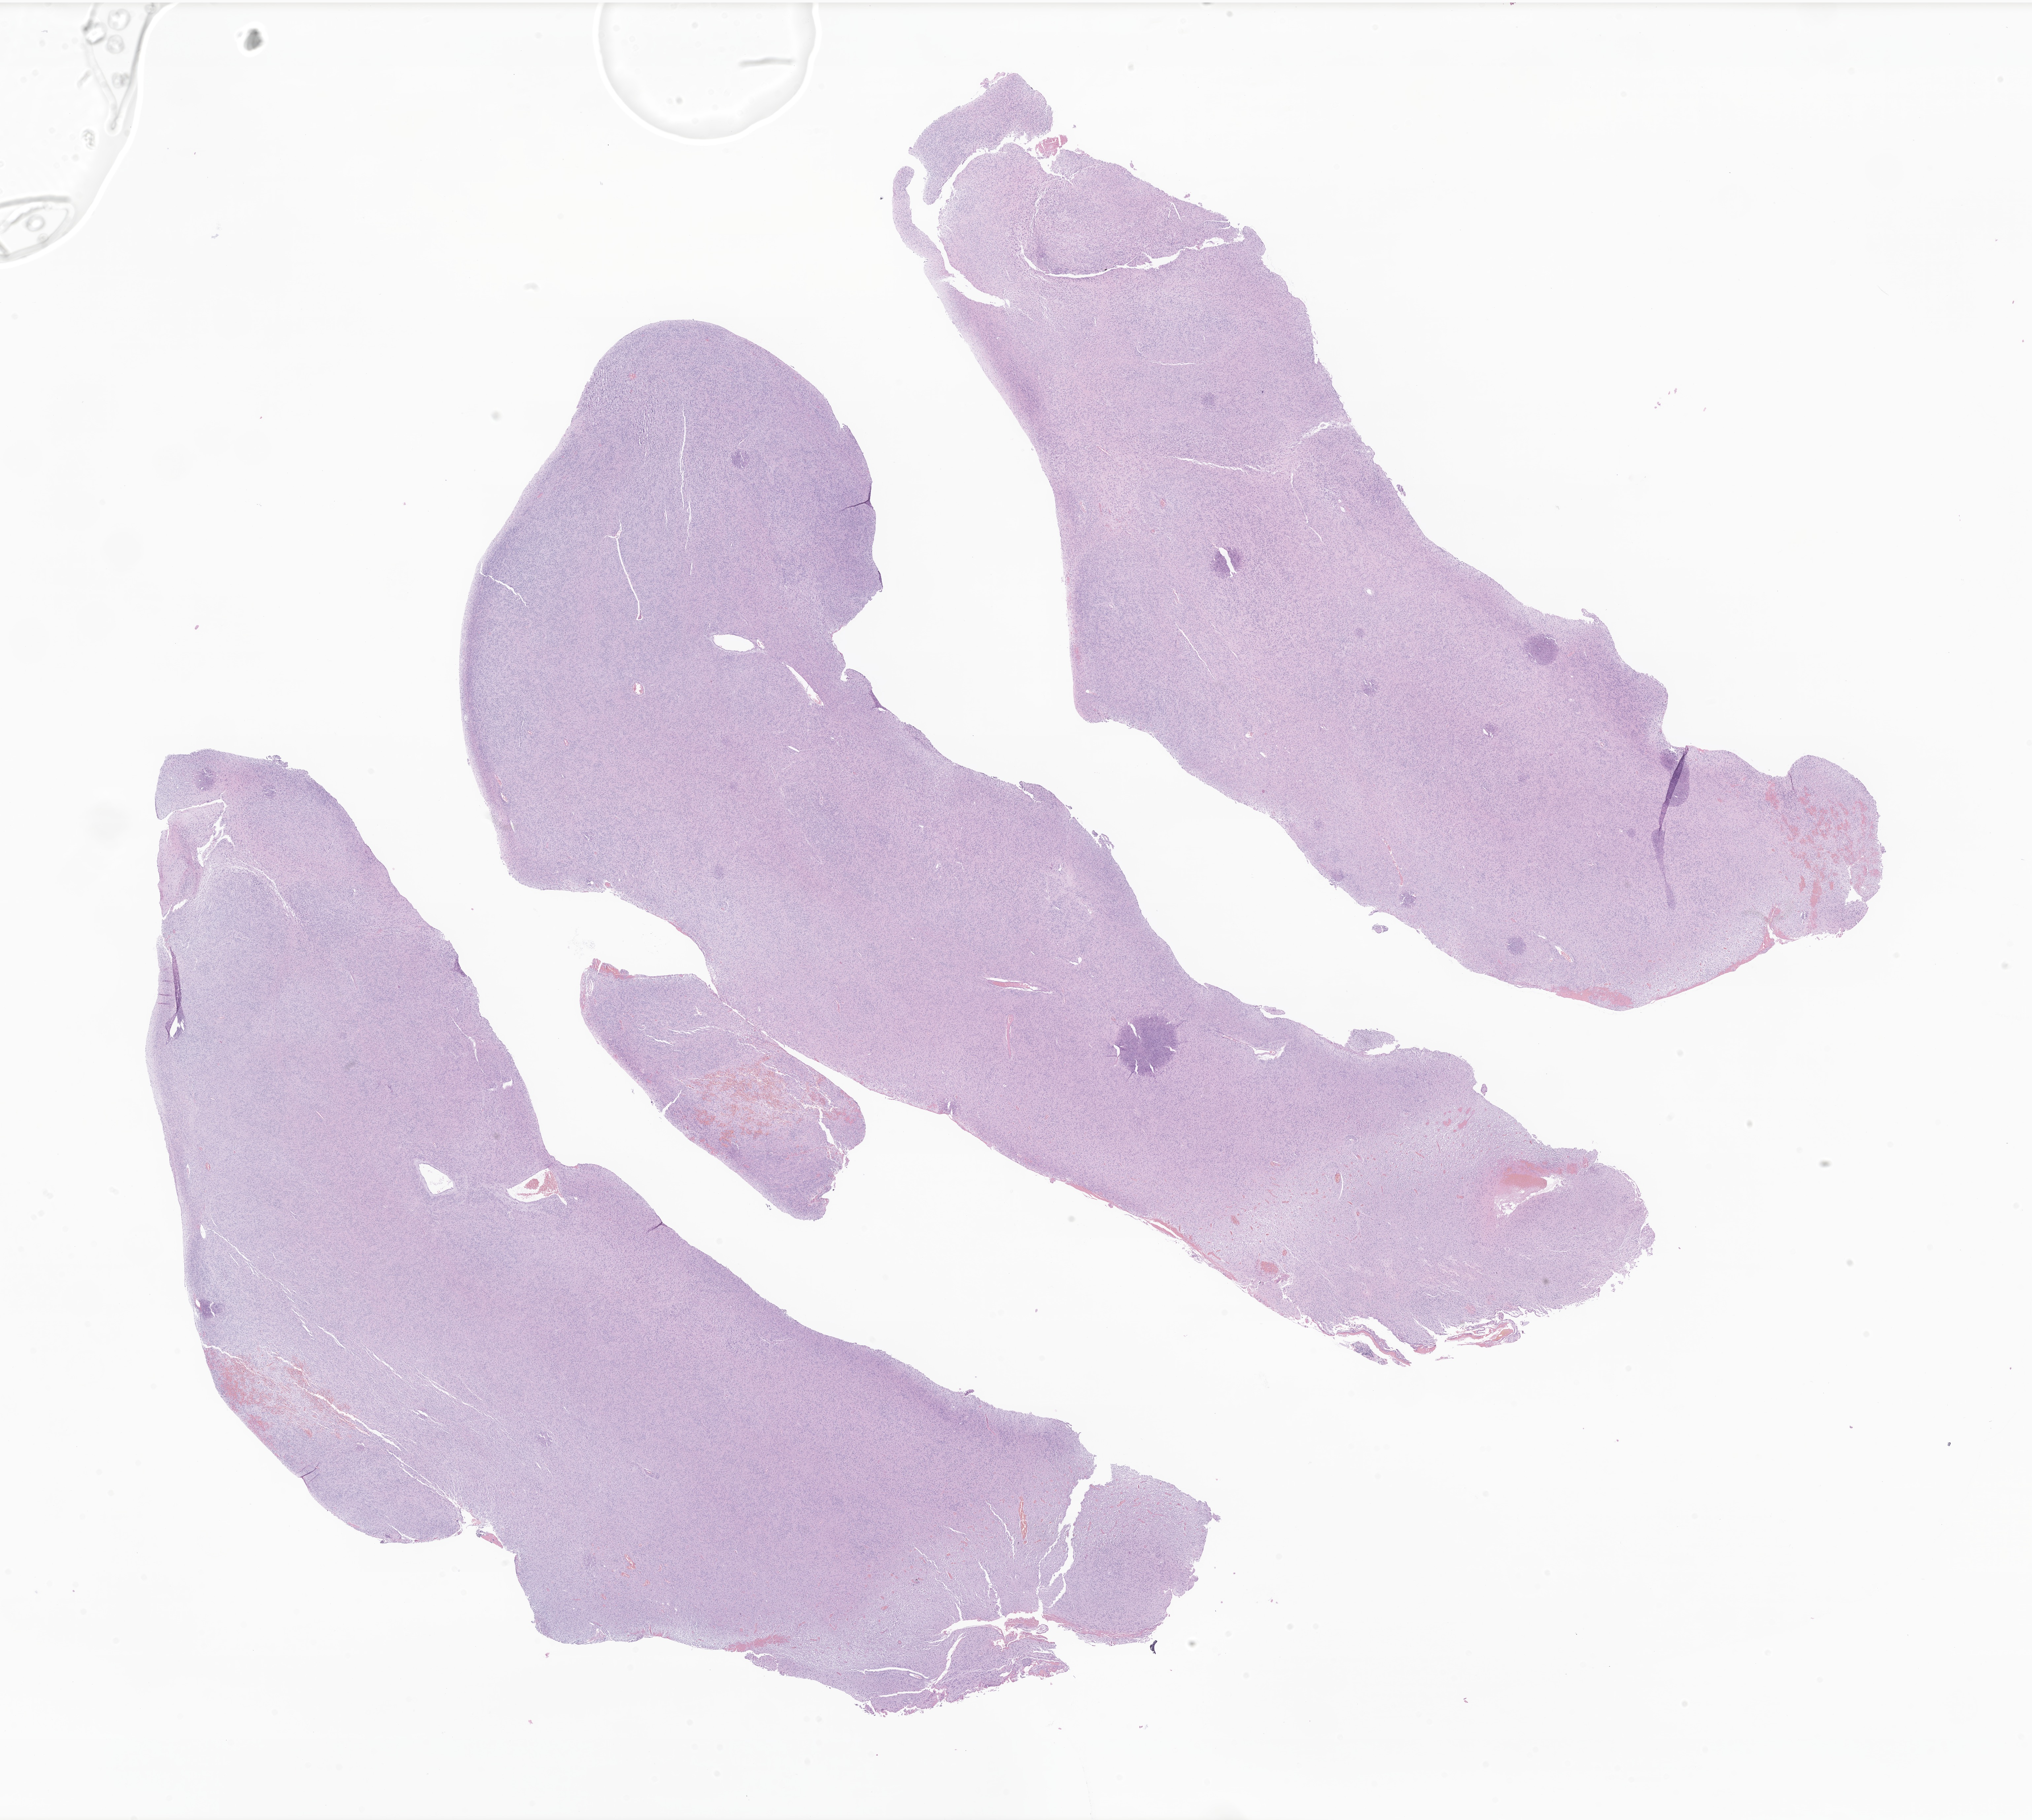
Digitized hematoxylin and eosin (H&E)-stained section of tumor tissue from the brain stem — low-resolution overview of the scanned area, about 25.9 x 23.2 mm, formalin-fixed paraffin-embedded section. Patient: male, age 956 days (about 2.6 years).
• diagnosis (ICD-O-3 morphology term): Ependymoma, anaplastic